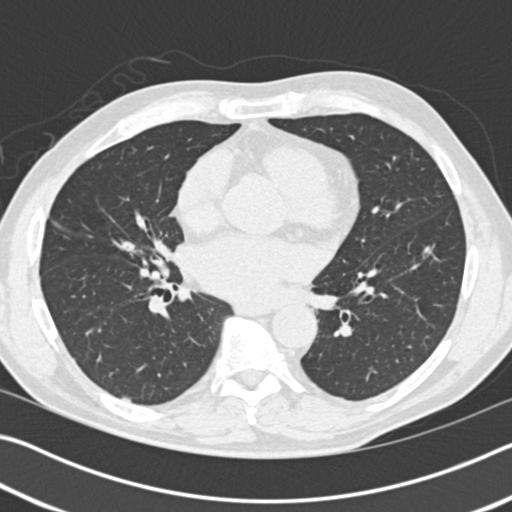
Chest CT (low-dose screening protocol), one axial image; baseline screening round; lung window (W 1500 / L -600 HU); 2 mm slice thickness; standard (soft-tissue) reconstruction kernel (B30f); 120 kVp; slice 92 of 193 in the series; 512 × 512 image matrix, field of view 340 × 340 mm. Male participant, aged 57 years at enrolment. Former smoker at enrolment.
Lesion marked by an expert reader, bounding box [x1, y1, x2, y2] px = [141, 246, 180, 285]. The screening reader recorded 2 non-calcified nodules or masses ≥4 mm on this exam (right middle lobe, right middle lobe); which of them this box marks is not recorded. Lung cancer was diagnosed 784 days after this screen (after the third annual screen): carcinoid tumor, NOS, right middle lobe, carcinoid, stage not assessed, 15 mm at pathology.